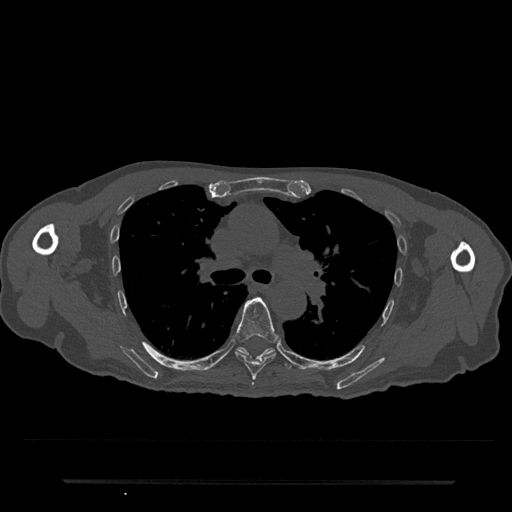
CT including the spine, one axial slice; slice 518 of 797 in the series (ordered by position); reconstruction kernel Br40s/3; 120 kVp; bone window (W 1800 / L 400 HU); 0.5 mm slice thickness; 512 × 512 image matrix, field of view 427 × 427 mm. Patient: male, 74 years. Case-level facts recorded for this patient, not image findings: primary cancer: prostate.
Outlined on this slice (semi-automatically segmented with operator editing):
- T6 vertebra: bounding box [x1, y1, x2, y2] px = [235, 297, 279, 380]
- T7 vertebra: [237, 347, 292, 369]